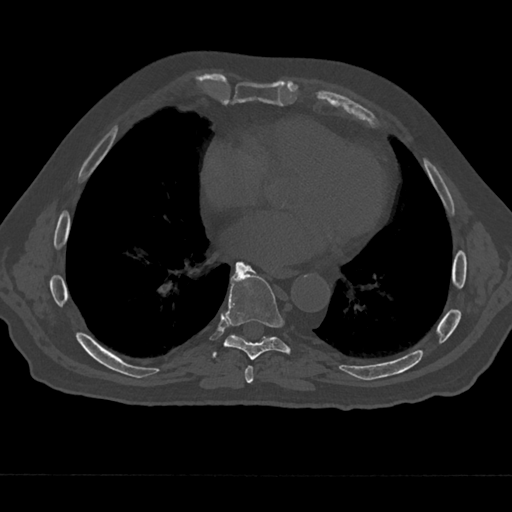
CT including the spine, one axial slice; slice 311 of 797 in the series (ordered by position); reconstruction kernel Br40s/3; bone window (W 1800 / L 400 HU); 512 × 512 image matrix, field of view 377 × 377 mm. Male patient, age 75 years. Case-level facts recorded for this patient, not image findings: primary cancer: renal.
Outlined on this slice (semi-automatic segmentation, software-assisted and operator-edited):
- T7 vertebra: bounding box [x1, y1, x2, y2] px = [240, 365, 254, 384]
- T8 vertebra: [212, 262, 291, 360]